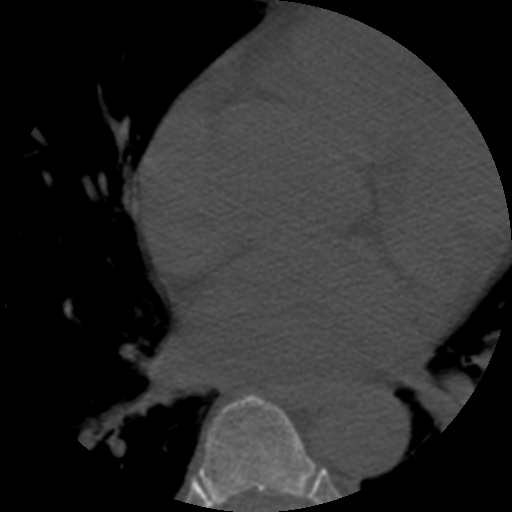
CT including the spine, one axial slice; position 347 of 508 along the scan axis; 120 kVp; bone window (W 1800 / L 400 HU); 1.25 mm slice thickness; 512 × 512 image matrix, field of view 160 × 160 mm. Patient age 57 years. From the clinical record (not read from this slice): primary cancer: prostate.
Annotated regions visible in this slice (semi-automatically segmented with operator editing):
- T6 vertebra: box from (x=197, y=394) to (x=323, y=512) px